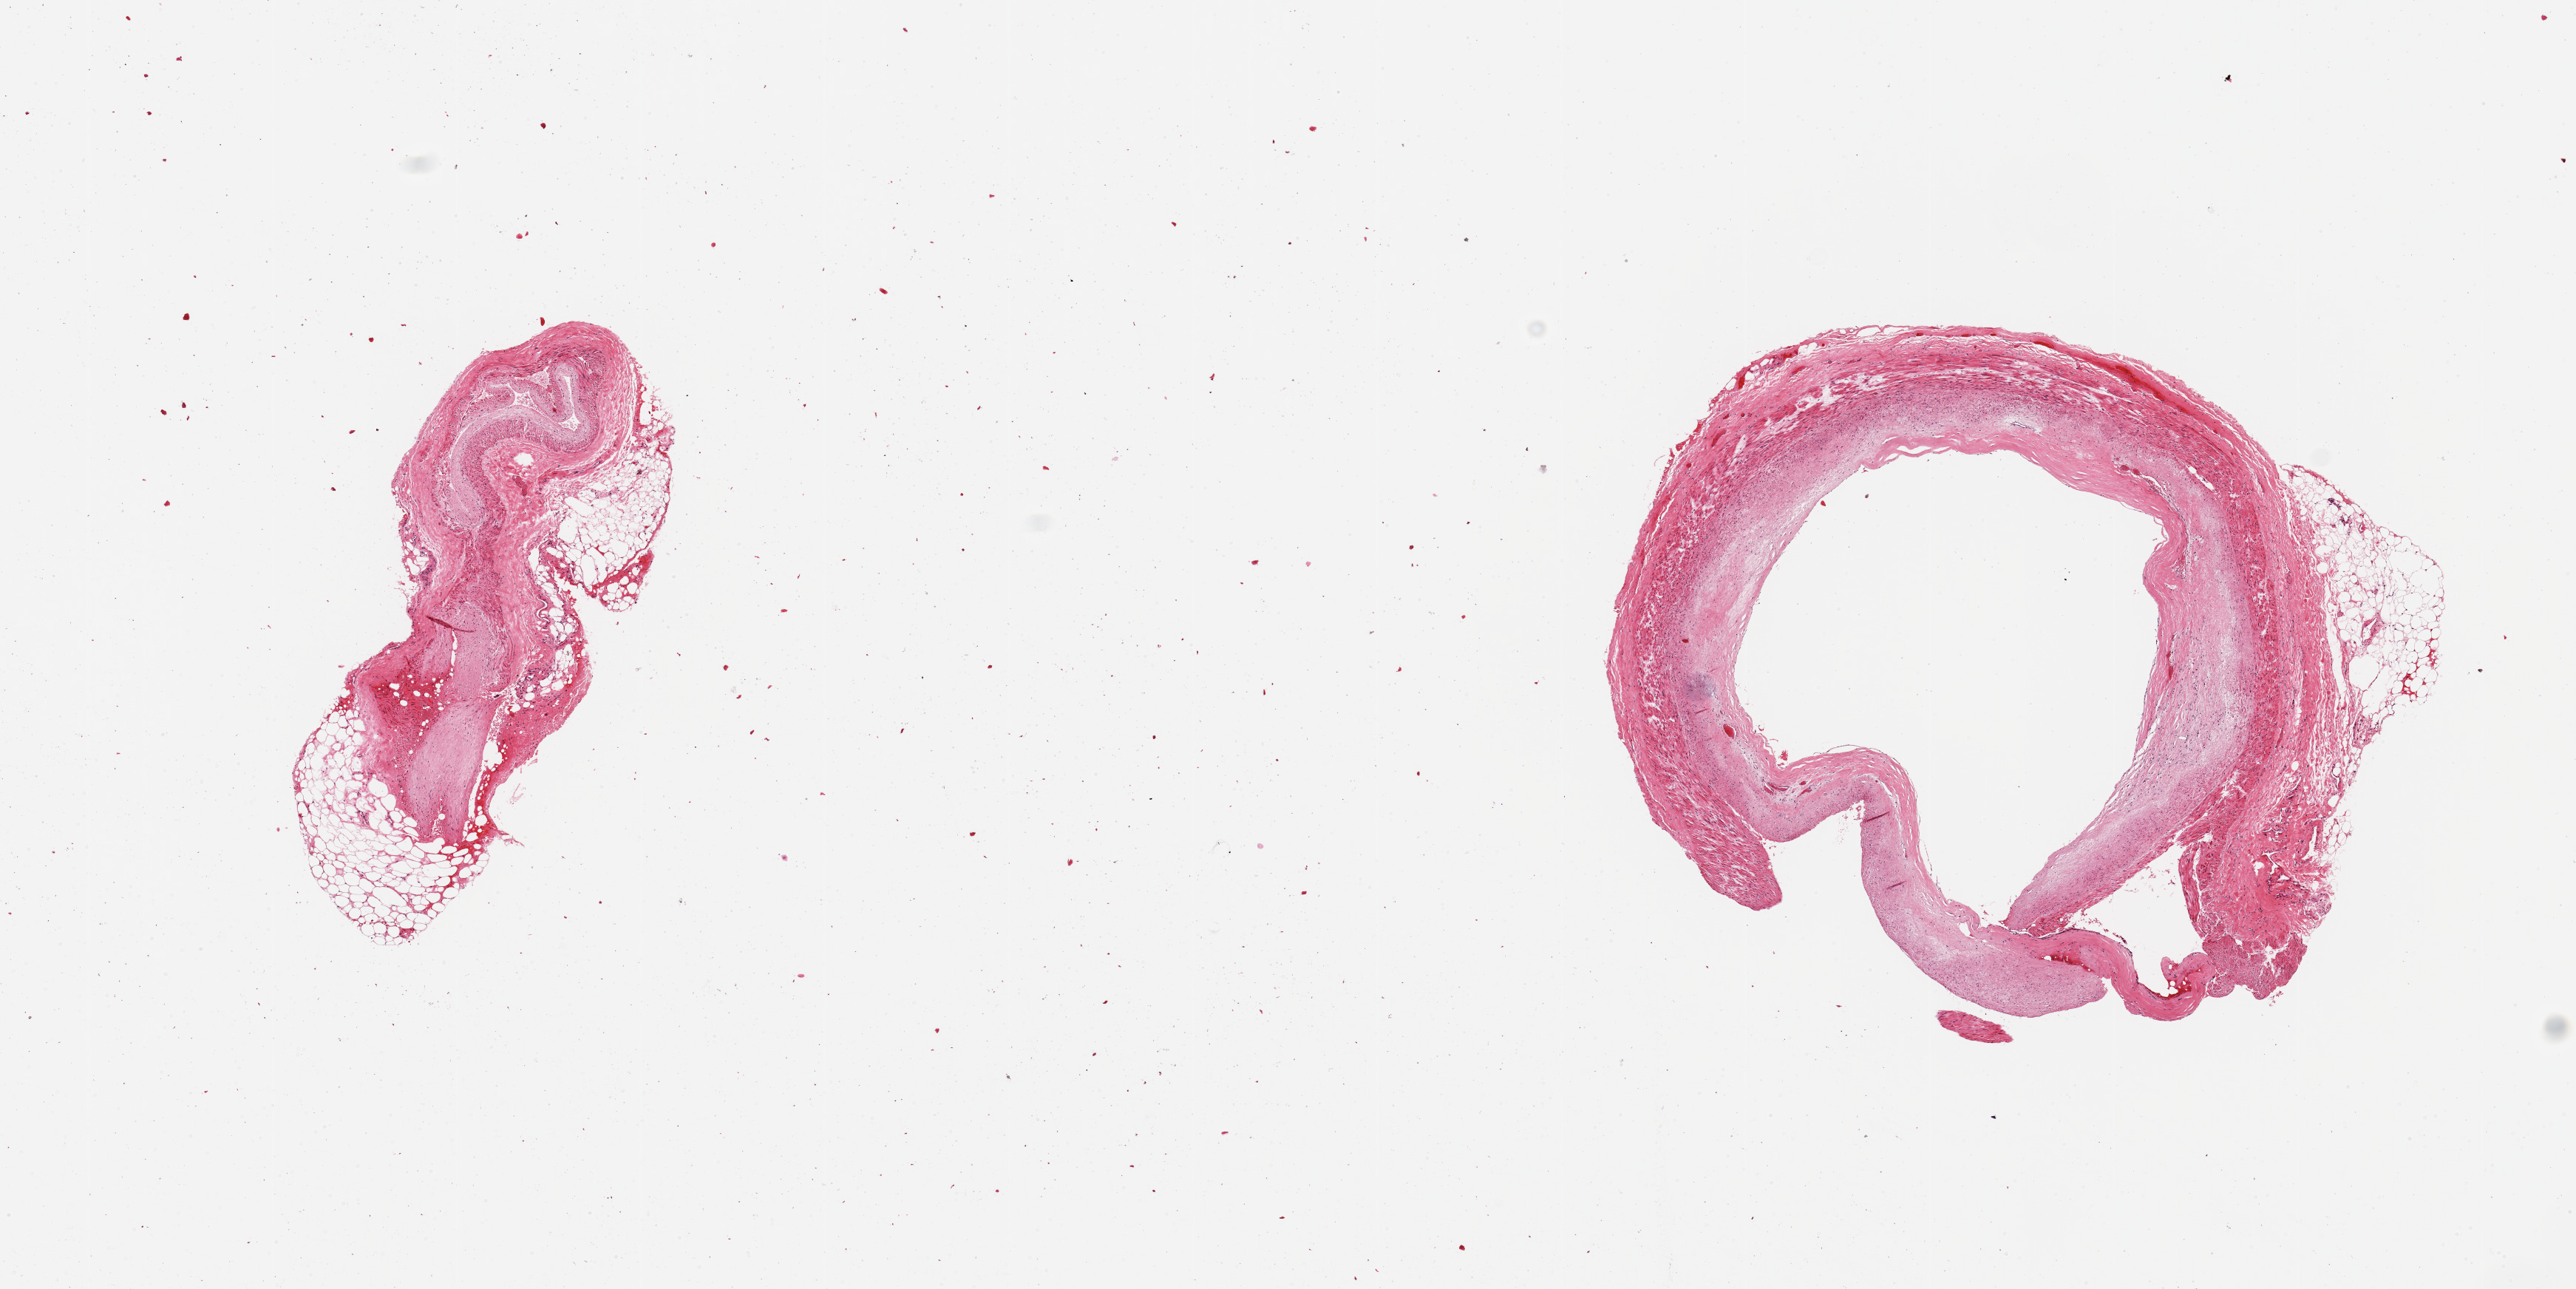
Digitized hematoxylin and eosin (H&E)-stained section, a low-resolution overview of the entire scanned area, about 13.8 x 6.9 mm; PAXgene-fixed paraffin-embedded (PFPE) section; section of coronary artery (target tissue); donor tissue sample. Donor: female.
* pathologist's review note for this sample: 2 pieces; atherosclerosis with up to 25% luminal narrowing in one piece; external fat up to 683 um